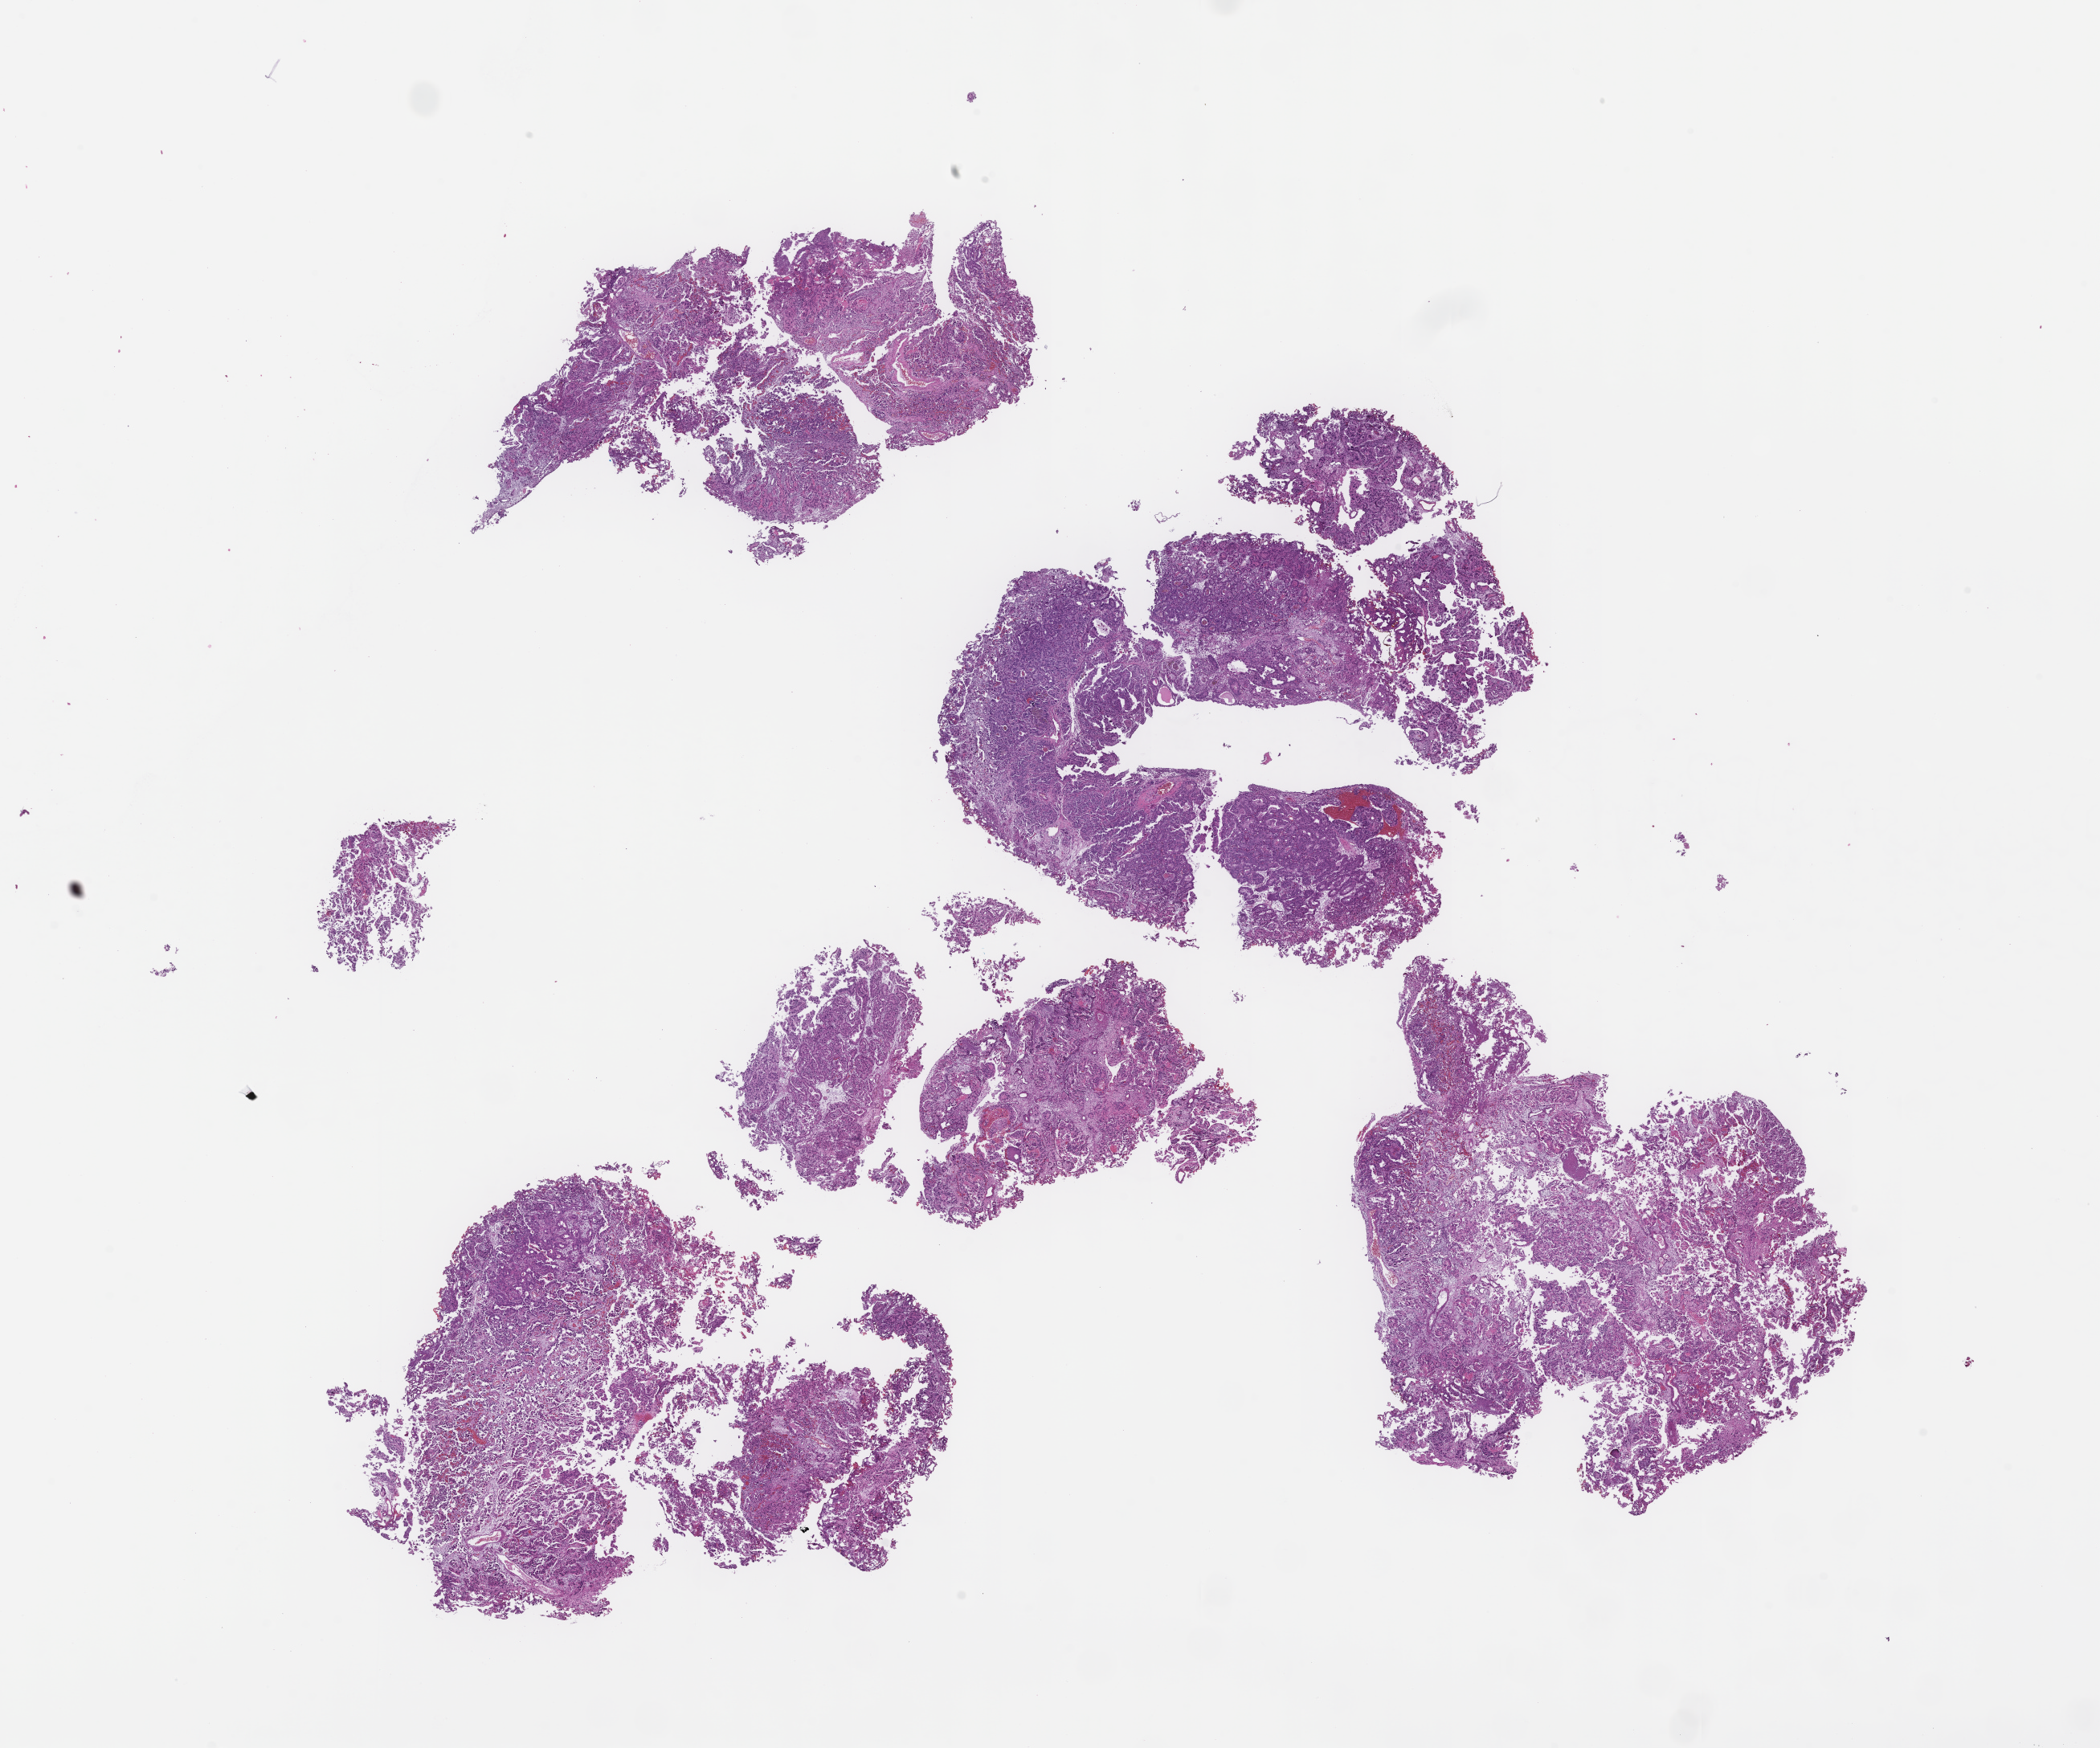
Whole-slide image, haematoxylin and eosin stain, whole scanned area (about 21.1 x 17.6 mm) shown as a low-resolution overview; formalin-fixed, paraffin-embedded (FFPE) tissue; archival tissue. Patient sex: male.
This section: metastasis (sampled organ not recorded). Patient diagnosis (primary): Prostate Carcinoma.